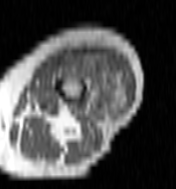
MRI of an extremity soft-tissue mass, one axial slice. MR volume resampled by the dataset authors to the PET/CT grid (not the native acquisition matrix). 176 × 189 image matrix. Female patient. Case-level facts recorded for this patient, not image findings: histological type: undifferentiated – high grade; grade: high; site of the primary tumour: left thigh.
Outlined on this slice (expert contour drawn on MRI and transferred to this co-registered scan by the dataset authors):
- gross tumour volume including surrounding oedema: bounding box [x1, y1, x2, y2] px = [64, 54, 125, 115]